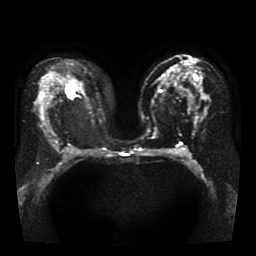
Breast MRI, one axial slice; slice 23 of 41 in the series (ordered by position); diffusion-weighted series; image 2 of 4 stored at this slice position (different b-values; order by instance number); 1.5 T; 5 mm slice thickness; 256 × 256 image matrix, field of view 330 × 330 mm. Female patient.
Structures marked on this image (outlined manually by an expert reader):
- tumour on diffusion-weighted imaging: box from (x=67, y=88) to (x=74, y=98) px